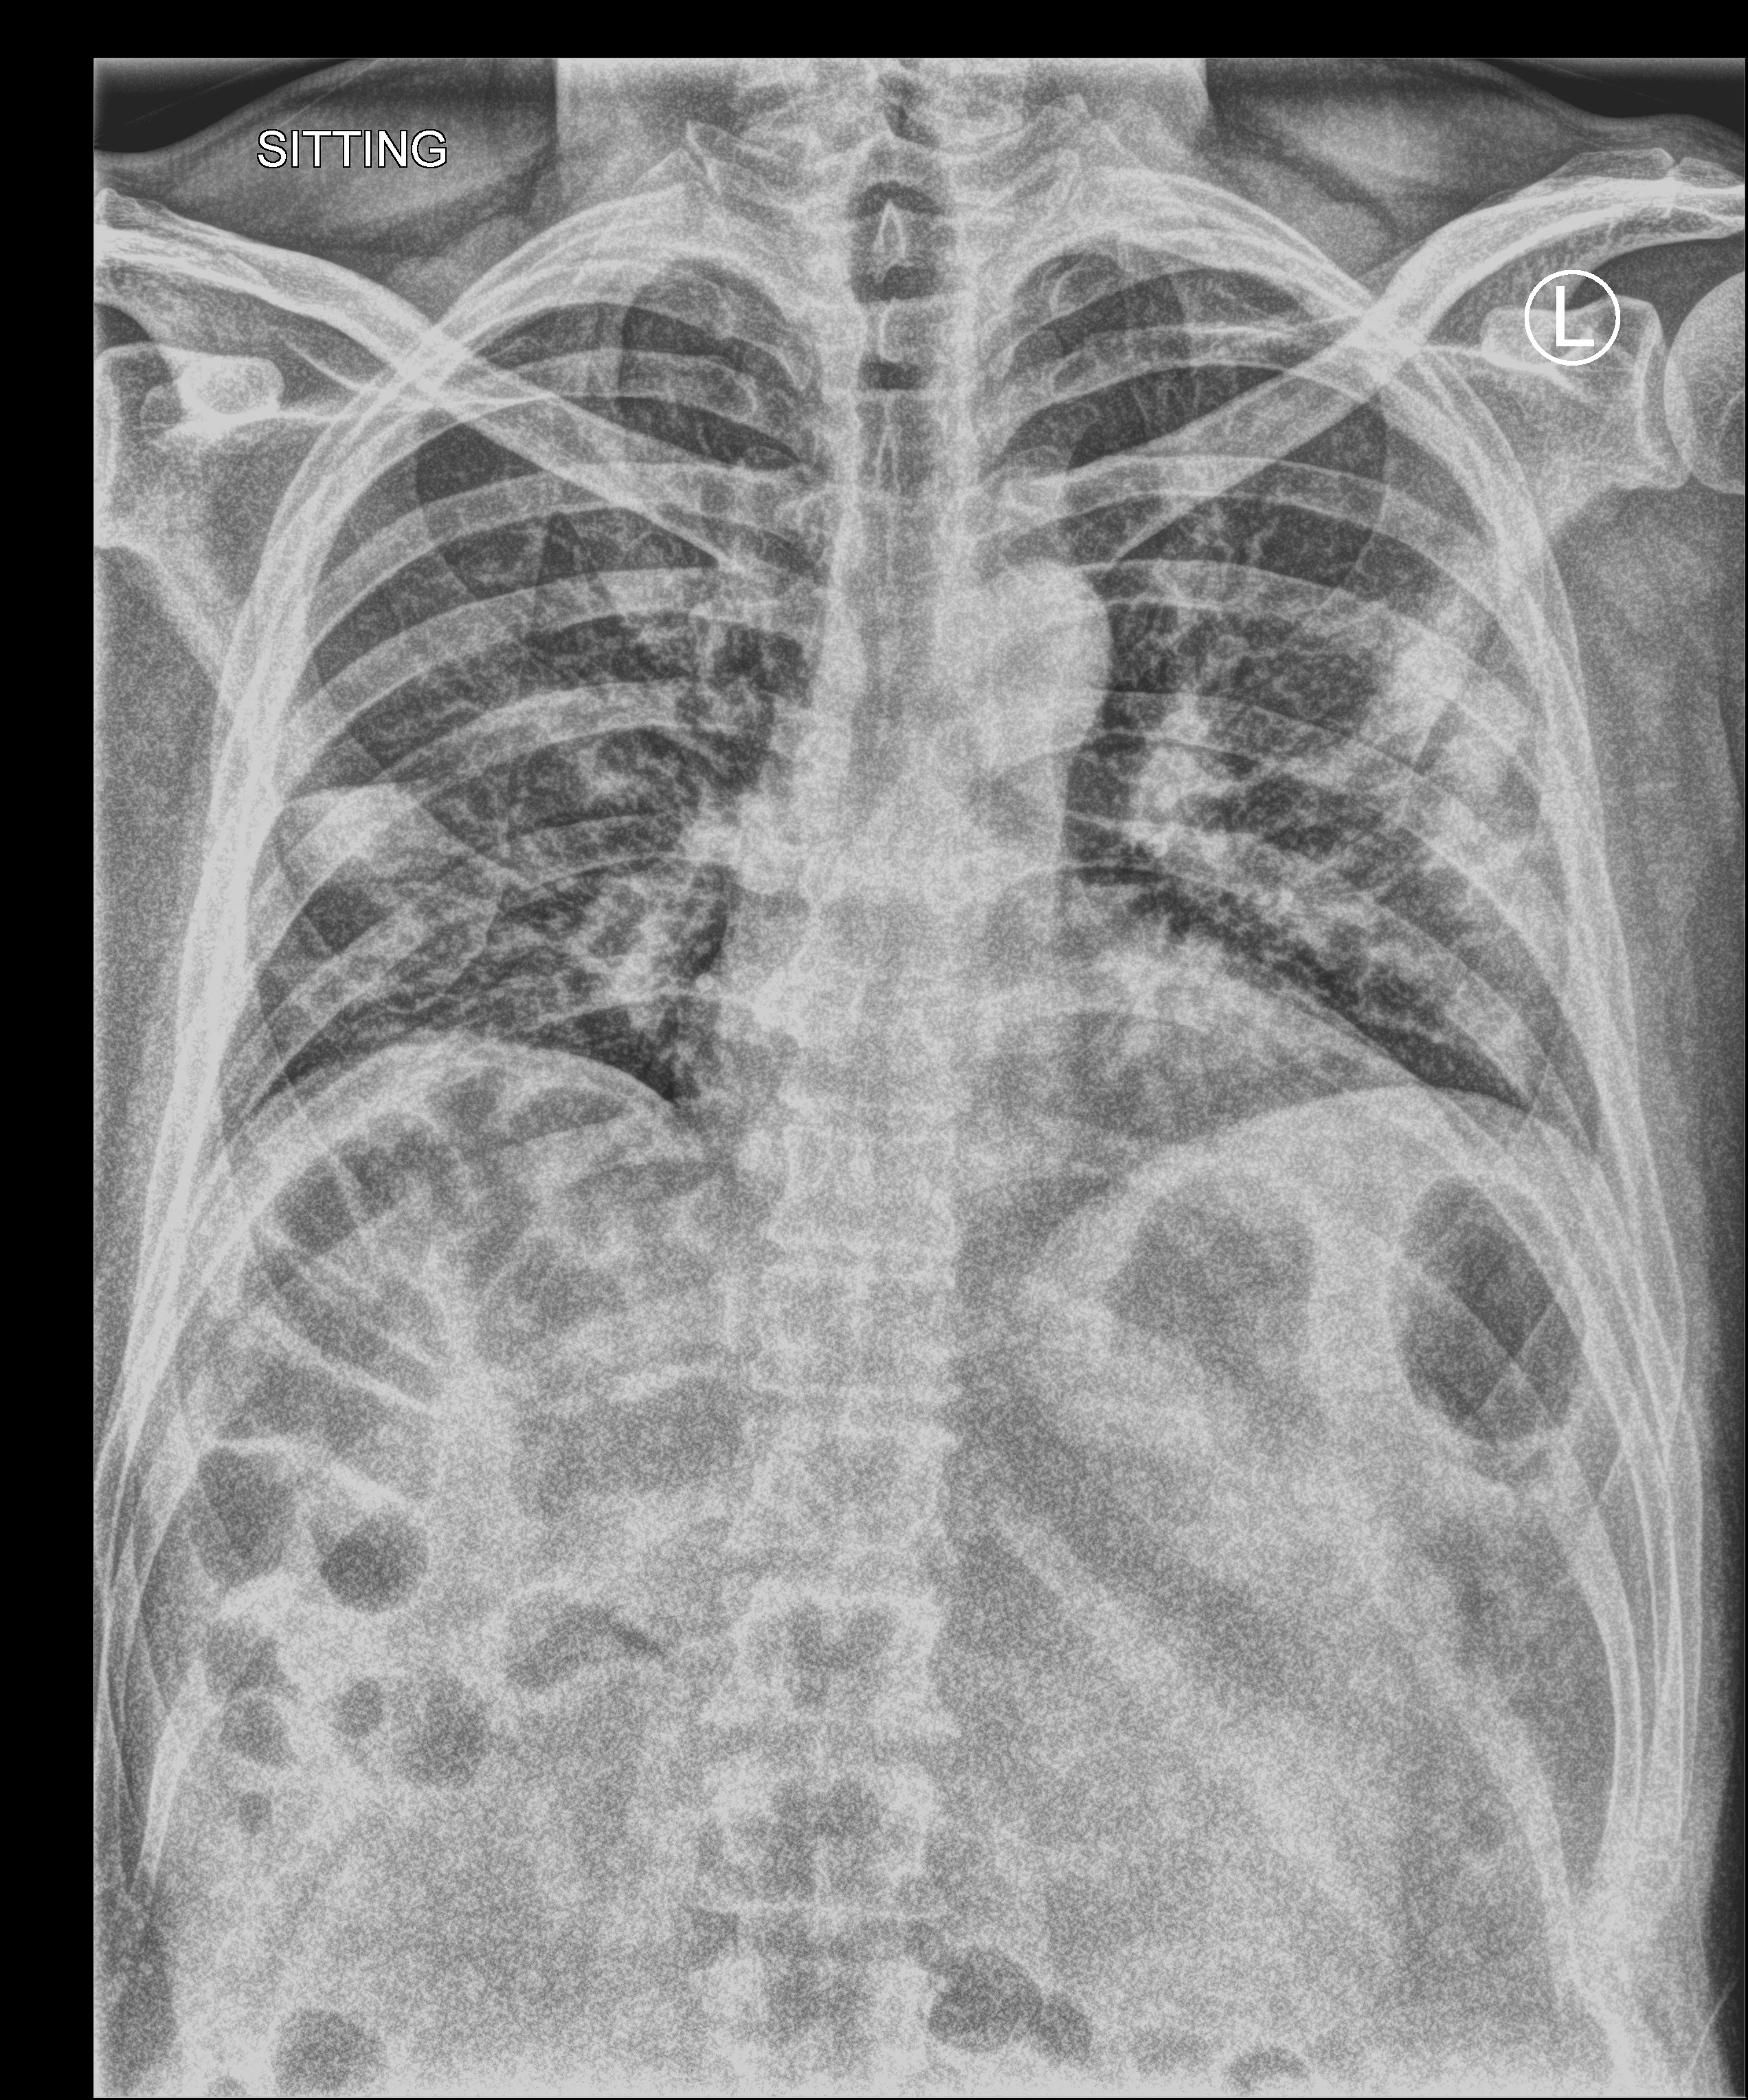
Portable chest radiograph, anteroposterior (AP) projection. Male patient hospitalised with COVID-19, age 18–59 years.
Hospital-stay facts (about this admission, not read from this image; timing relative to this image not recorded):
- length of hospital stay: 1 day
- admitted to intensive care during this hospital stay: no